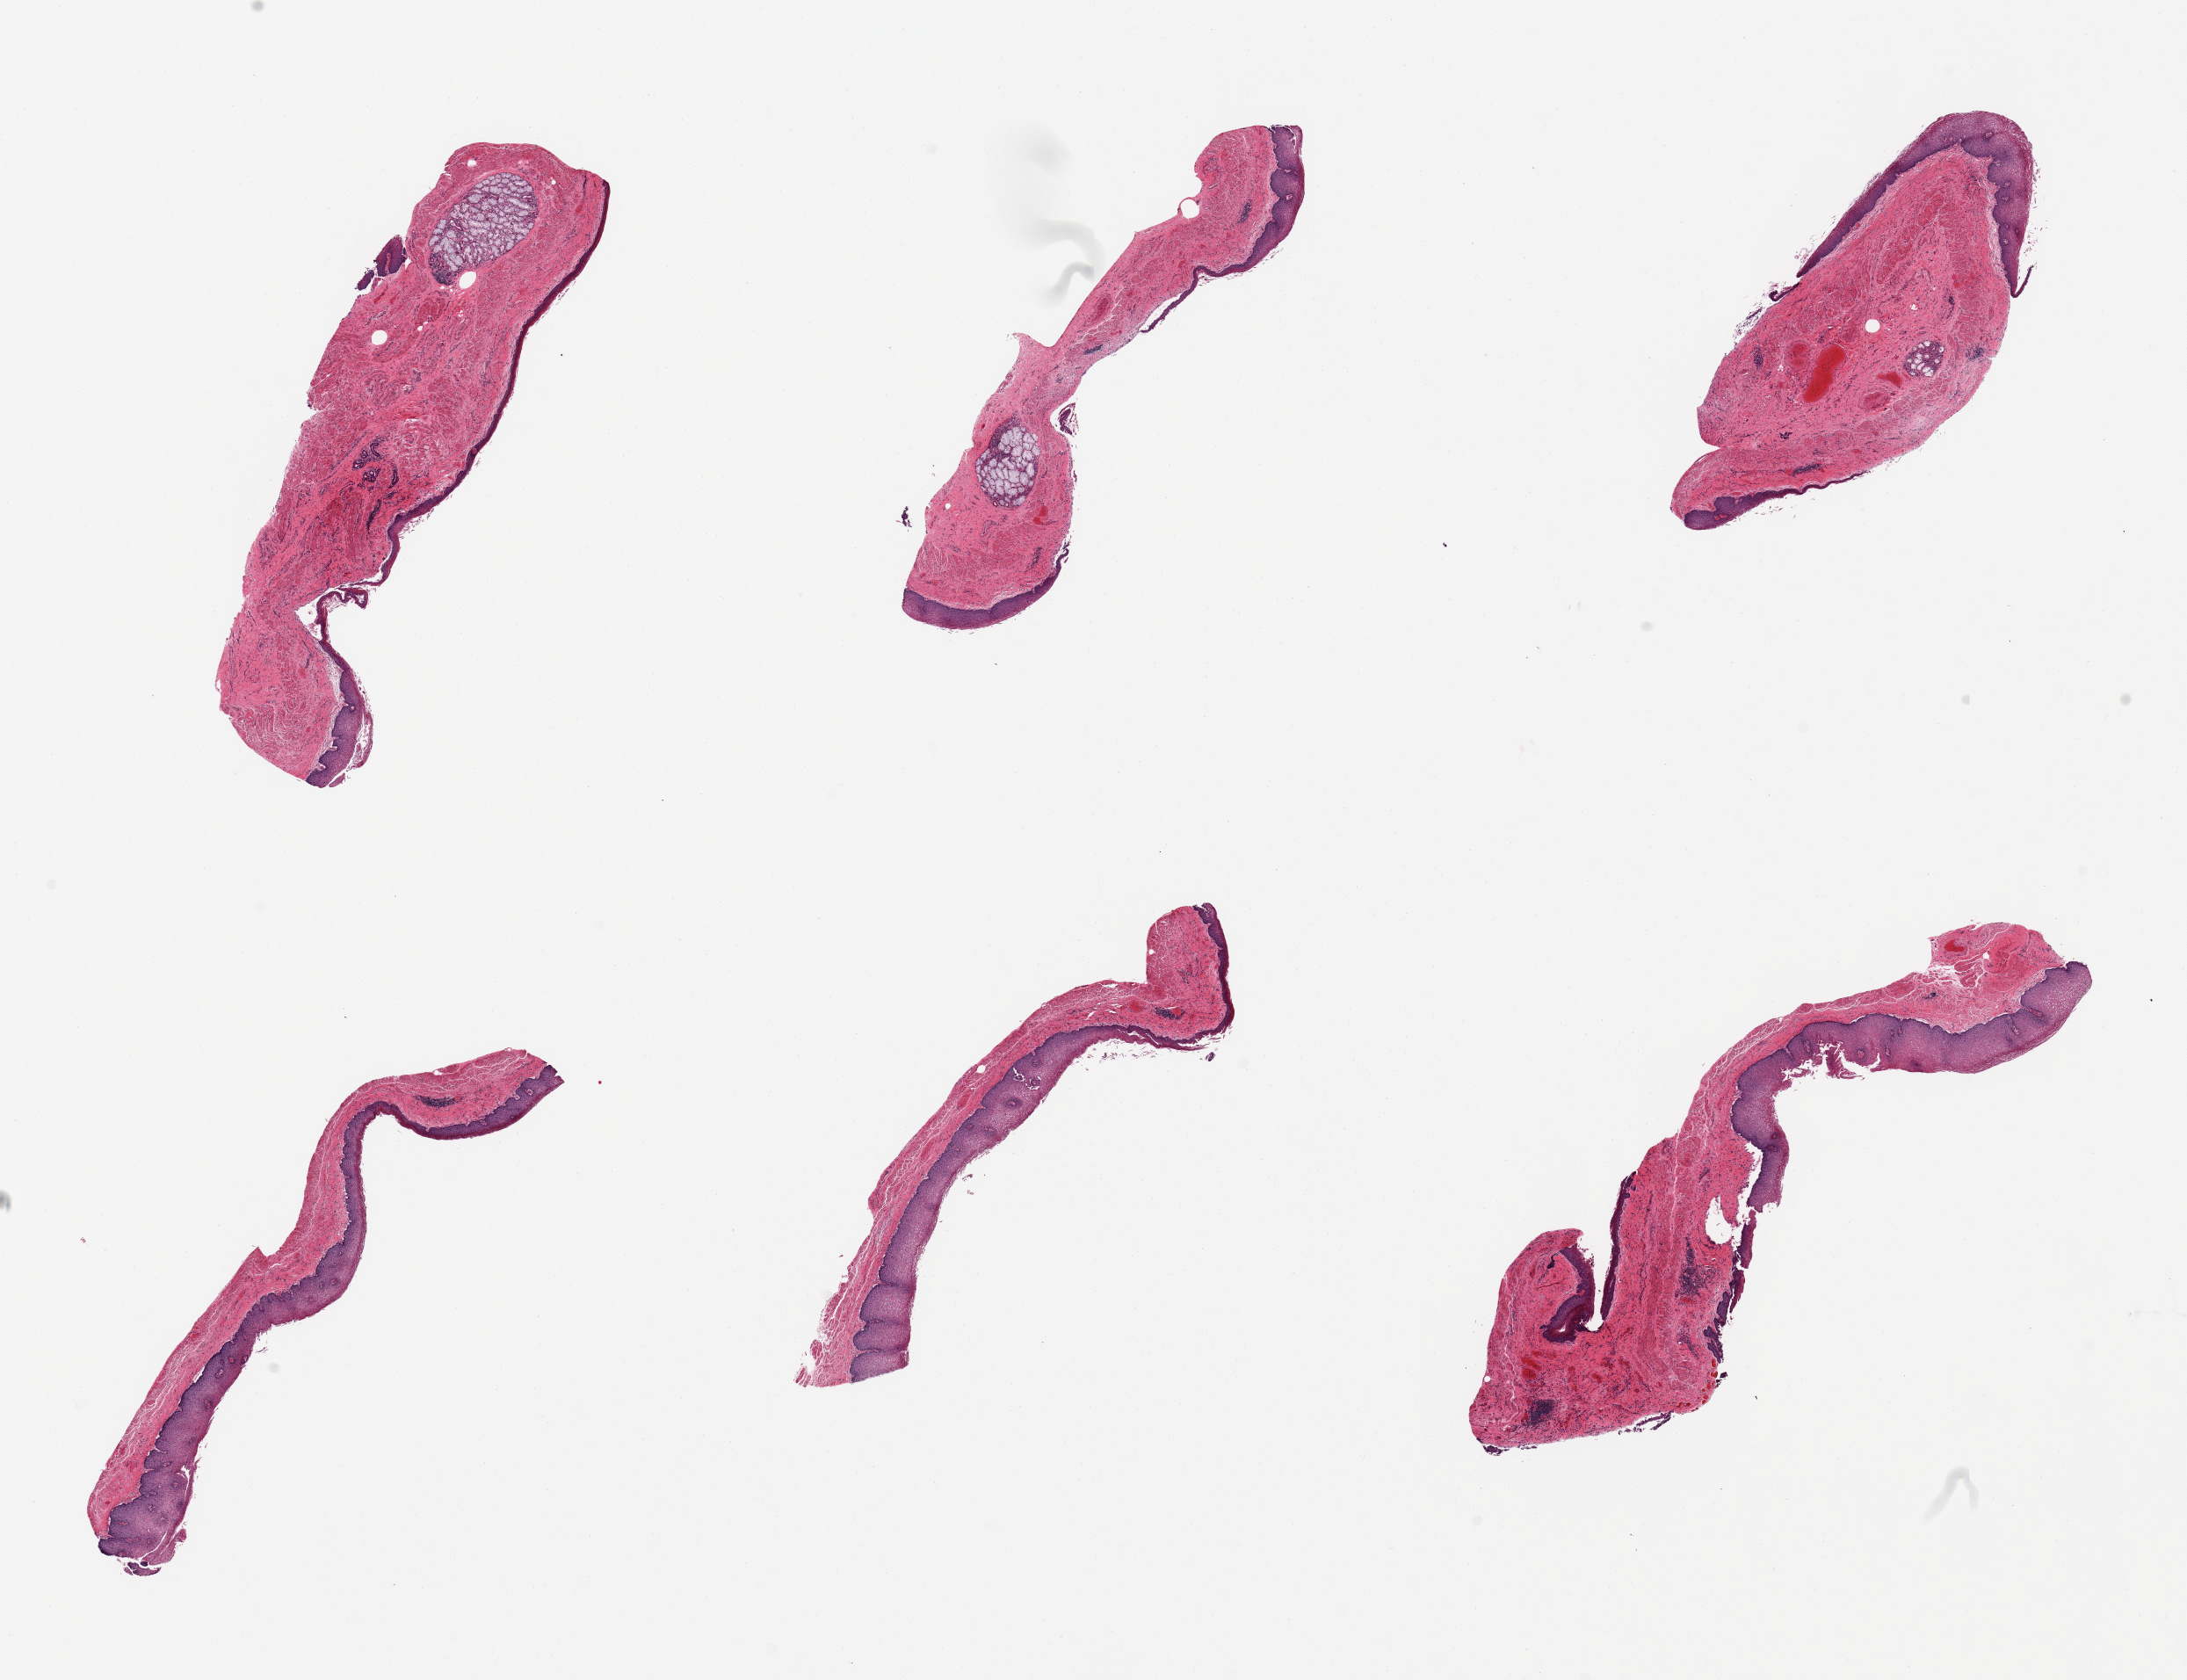
Whole-slide image, hematoxylin and eosin (H&E) stain, a low-resolution overview of the entire scanned area, about 19.7 x 15.1 mm, PAXgene-fixed, paraffin-embedded tissue, sampled site (target tissue): esophageal mucous membrane, donor tissue sample. Donor: male.
Pathologist's review note for this sample: 6 pieces; slightly fragmented epithelium.